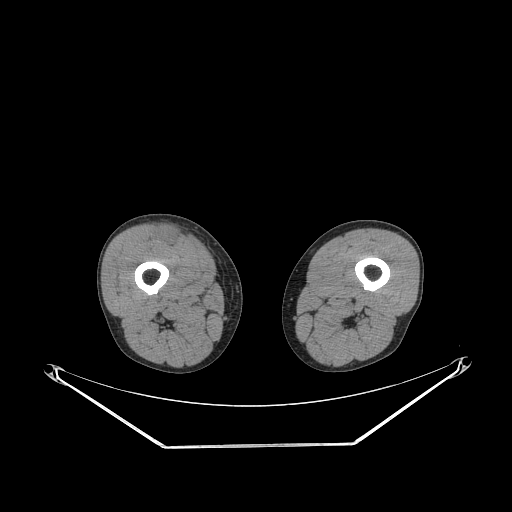
CT of an extremity soft-tissue mass (from a PET/CT study), one axial slice; position 232 of 311 along the scan axis; reconstruction kernel STANDARD; 140 kVp; soft-tissue window (W 400 / L 40 HU); 3.75 mm slice thickness; 512 × 512 image matrix, field of view 500 × 500 mm. Male patient. From the clinical record (not read from this slice): histological type: pleiomorphic leiomyosarcoma; grade: intermediate; site of the primary tumour: right thigh.
Outlined on this slice (expert contour drawn on MRI and transferred to this co-registered scan by the dataset authors):
- gross tumour volume including surrounding oedema: box from (x=157, y=230) to (x=181, y=245) px